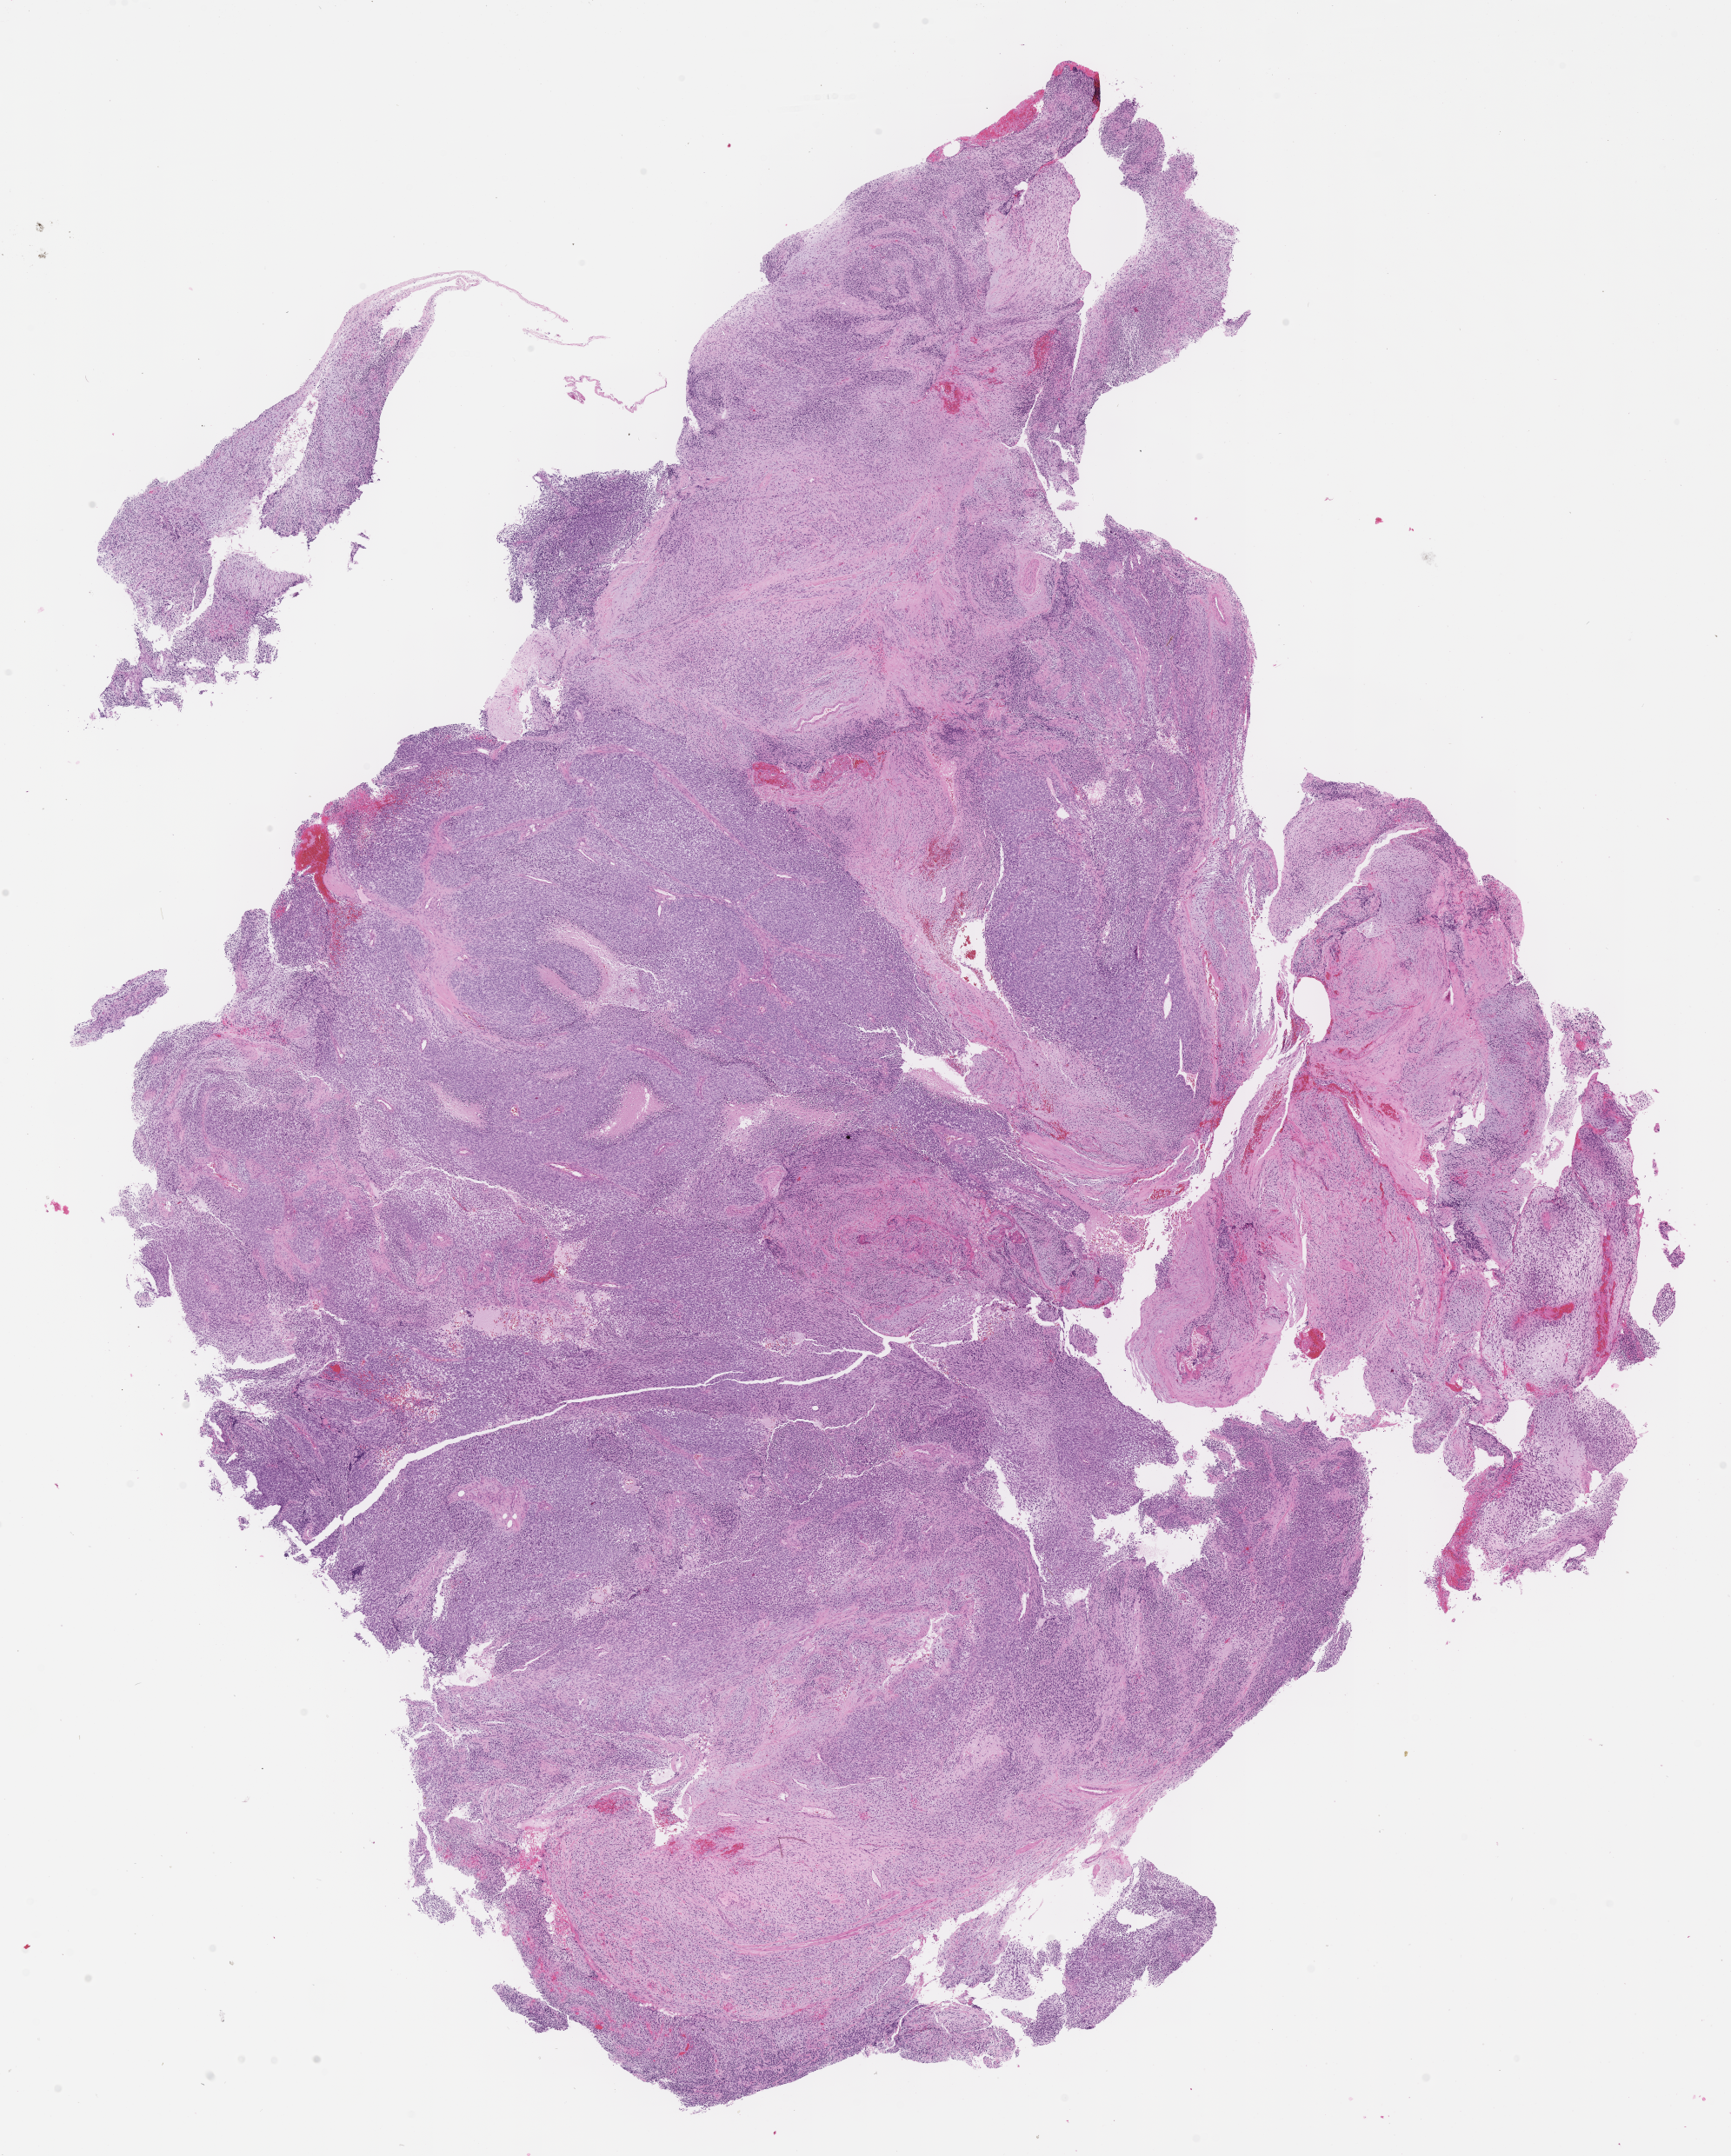
Digitized hematoxylin and eosin (H&E)-stained section of tumor tissue, whole scanned area (about 16.1 x 20.1 mm) shown as a low-resolution overview, formalin-fixed, paraffin-embedded (FFPE) tissue, site: pelvis. Patient: female, age 8.4 years at diagnosis.
Diagnosis: rhabdomyosarcoma; histological classification: embryonal rhabdomyosarcoma. Stage (as recorded): 4. Metastatic status at presentation (as recorded): metastatic (confirmed).